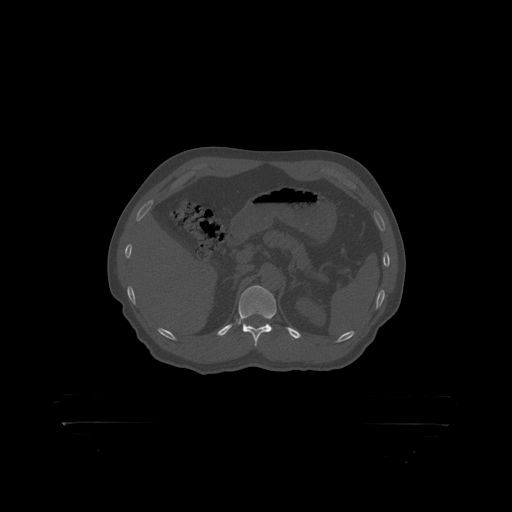
CT including the spine, one axial slice; slice 349 of 399 in the series (ordered by position); 120 kVp; bone window (W 1800 / L 400 HU); 512 × 512 image matrix. Male patient, age 46 years. From the clinical record (not read from this slice): primary cancer: skin.
Annotated regions visible in this slice (semi-automatically segmented with operator editing):
- T12 vertebra: box from (x=239, y=286) to (x=277, y=319) px